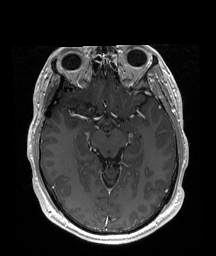
Brain MRI from a brain-tumour surgery series, one axial slice; position 116 of 192 along the scan axis; T1-weighted post-contrast; 216 × 256 image matrix, field of view 219 × 260 mm. Case-level facts recorded for this patient, not image findings: histopathology: Astrocytoma; WHO grade: 2; IDH mutation: yes; tumour location: Right Insular.
Structures marked on this image (manually delineated by an expert):
- tumour: bounding box (x1, y1, x2, y2) in pixels: (67, 97, 91, 131)